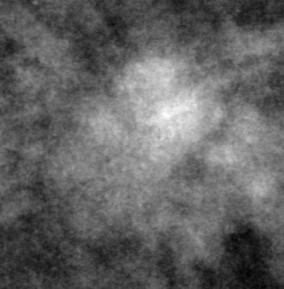
Region of interest cut from a scanned film mammogram (one marked finding), right breast, CC view, BI-RADS breast density category 2 (scale 1–4).
Marked abnormality: mass, shape oval, margins ill defined; BI-RADS assessment category 4; pathology (as recorded): benign.